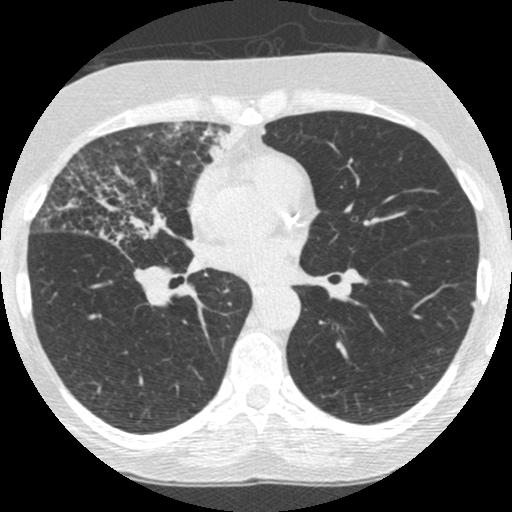
Low-dose screening chest CT, one axial slice. Position 132 of 253 along the scan axis. Reconstruction kernel STANDARD. 120 kVp. Lung window (W 1500 / L -600 HU). 1.25 mm slice thickness. 512 × 512 image matrix, field of view 294 × 294 mm.
Annotated regions visible in this slice (manually delineated by an expert):
- lesion 4 (tumor, upper lobe of right lung): bounding box (x1, y1, x2, y2) in pixels: (198, 124, 246, 161)